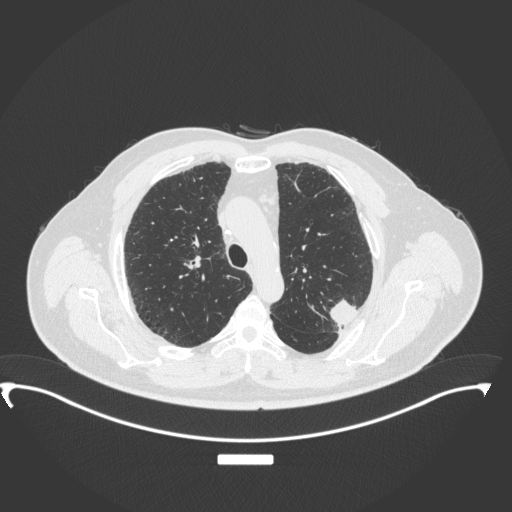
Chest CT, one axial slice; slice 263 of 350 in the series (ordered by position); reconstruction kernel B31f; 120 kVp; lung window (W 1500 / L -600 HU); 1 mm slice thickness; 512 × 512 image matrix, field of view 459 × 459 mm. Male patient, age 64 years. From the clinical record (not read from this slice): clinical TNM (as recorded): T1c N1 M1.
Annotated regions visible in this slice (rectangle marked by the reading radiologist):
- lung tumour (recorded histology: adenocarcinoma): bounding box <321,292,360,330> (left, top, right, bottom; pixels)